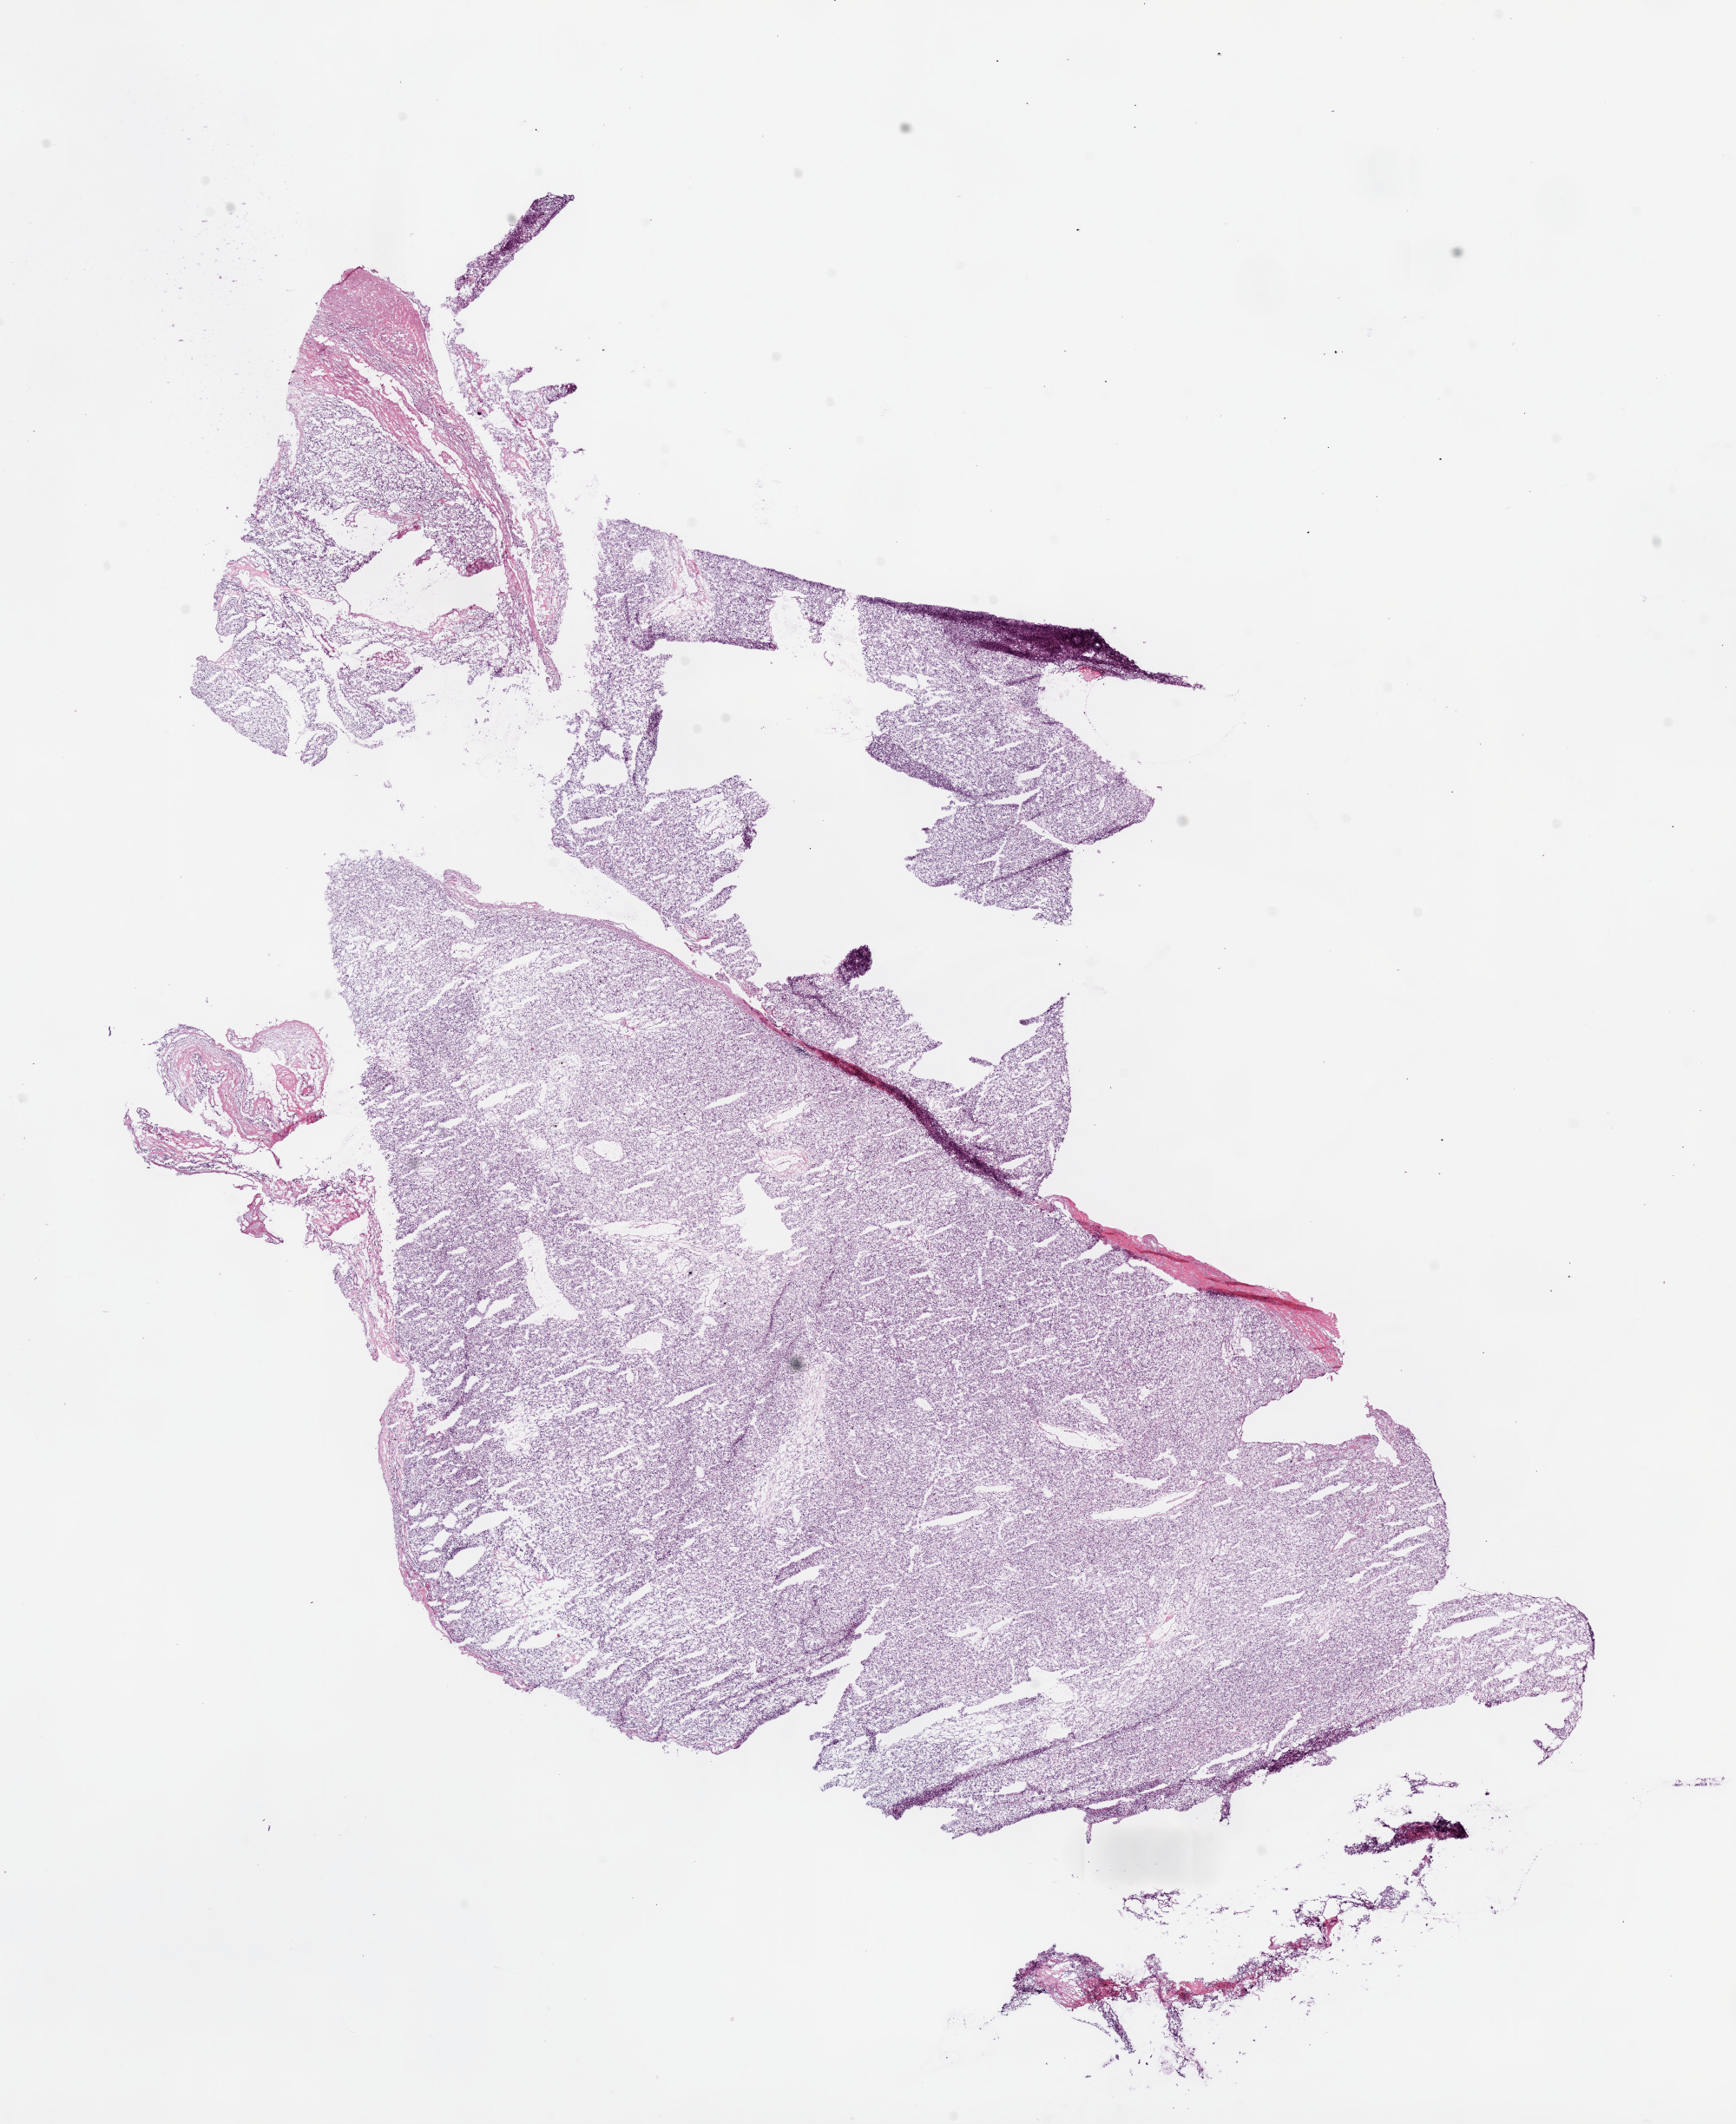
Hematoxylin and eosin (H&E) stained whole-slide image — shown as a low-resolution overview of the whole scanned area (about 16.0 x 19.6 mm, acquisition: 20x scan), frozen section, kidney, primary tumour sample. Patient: female, age at initial diagnosis 51 years. Histologic grade: G2 (moderately differentiated). Slide review estimates, as recorded: tumour cells 95%, tumour nuclei 85%, normal cells 0%, stromal cells 5%, necrosis 0%.
Lymph nodes positive (case pathology): 0 of 17 examined. AJCC pathologic stage: III. Histologic diagnosis: Clear cell adenocarcinoma, NOS.